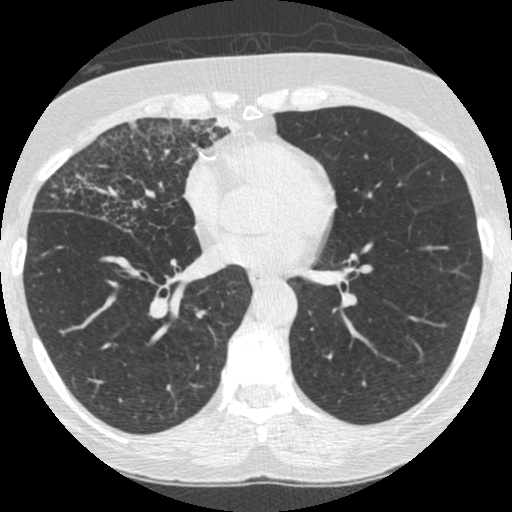
Low-dose screening chest CT, one axial slice; slice 120 of 253 in the series (ordered by position); 120 kVp; lung window (W 1500 / L -600 HU); 512 × 512 image matrix.
Annotated regions visible in this slice (manually delineated by an expert):
- lesion 4 (tumor, upper lobe of right lung): bounding box (x1, y1, x2, y2) in pixels: (183, 114, 240, 153)